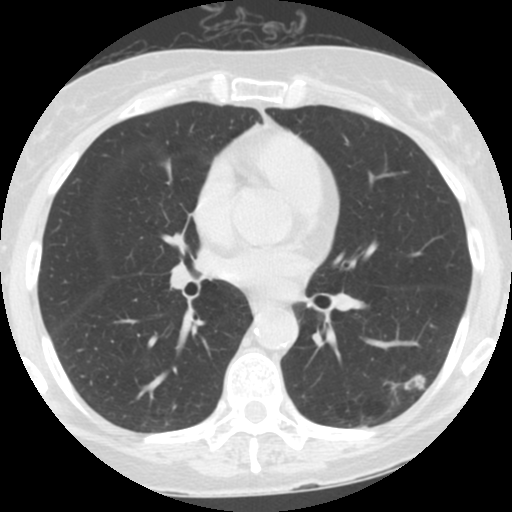
Low-dose screening chest CT, one axial slice; slice 70 of 152 in the series (ordered by position); reconstruction kernel STANDARD; 120 kVp; lung window (W 1500 / L -600 HU); 2.5 mm slice thickness; 512 × 512 image matrix, field of view 280 × 280 mm.
Outlined on this slice (manually delineated by an expert):
- lesion 1 (tumor, lower lobe of left lung): bounding box (x1, y1, x2, y2) in pixels: (402, 374, 426, 393)